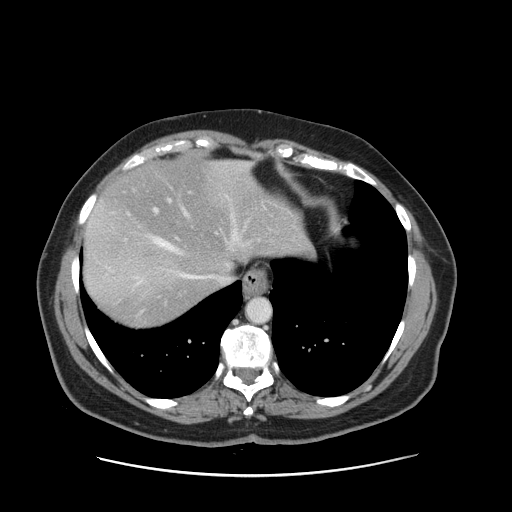
Contrast-enhanced abdominal CT, one axial slice; slice 128 of 161 in the series (ordered by position); 120 kVp; intravenous contrast given; soft-tissue window (W 400 / L 40 HU); 2.5 mm slice thickness; 512 × 512 image matrix, field of view 398 × 398 mm. Female patient, age 62 years. Case-level facts recorded for this patient, not image findings: diagnosis: colorectal cancer liver metastases, imaged before liver resection; multiple liver metastases: no; largest metastasis: 2.5 cm; disease in both lobes: no.
Outlined on this slice (expert manual segmentation):
- hepatic veins: bounding box <109,163,250,286> (left, top, right, bottom; pixels)
- liver: <83,161,305,327>
- planned liver remnant (the part of the liver to remain after resection): <94,161,304,279>
- portal vein (with intrahepatic branches): <154,191,191,241>